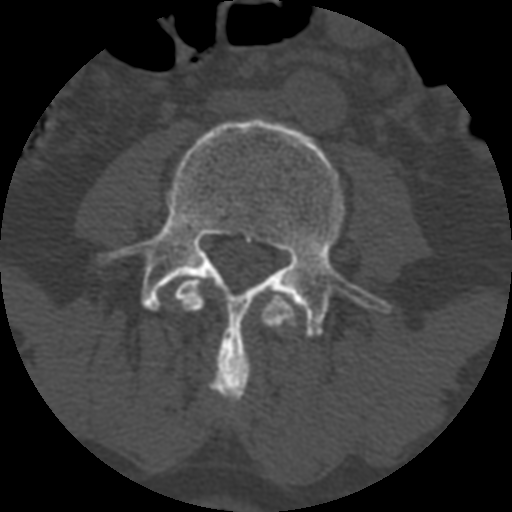
CT including the spine, one axial slice. Slice 287 of 399 in the series (ordered by position). 120 kVp. Bone window (W 1800 / L 400 HU). 1.25 mm slice thickness. 512 × 512 image matrix. Patient age 71 years. From the clinical record (not read from this slice): primary cancer: prostate.
Annotated regions visible in this slice (semi-automatically segmented with operator editing):
- L3 vertebra: box from (x=170, y=277) to (x=297, y=330) px
- L4 vertebra: (x=99, y=118)–(x=390, y=404)